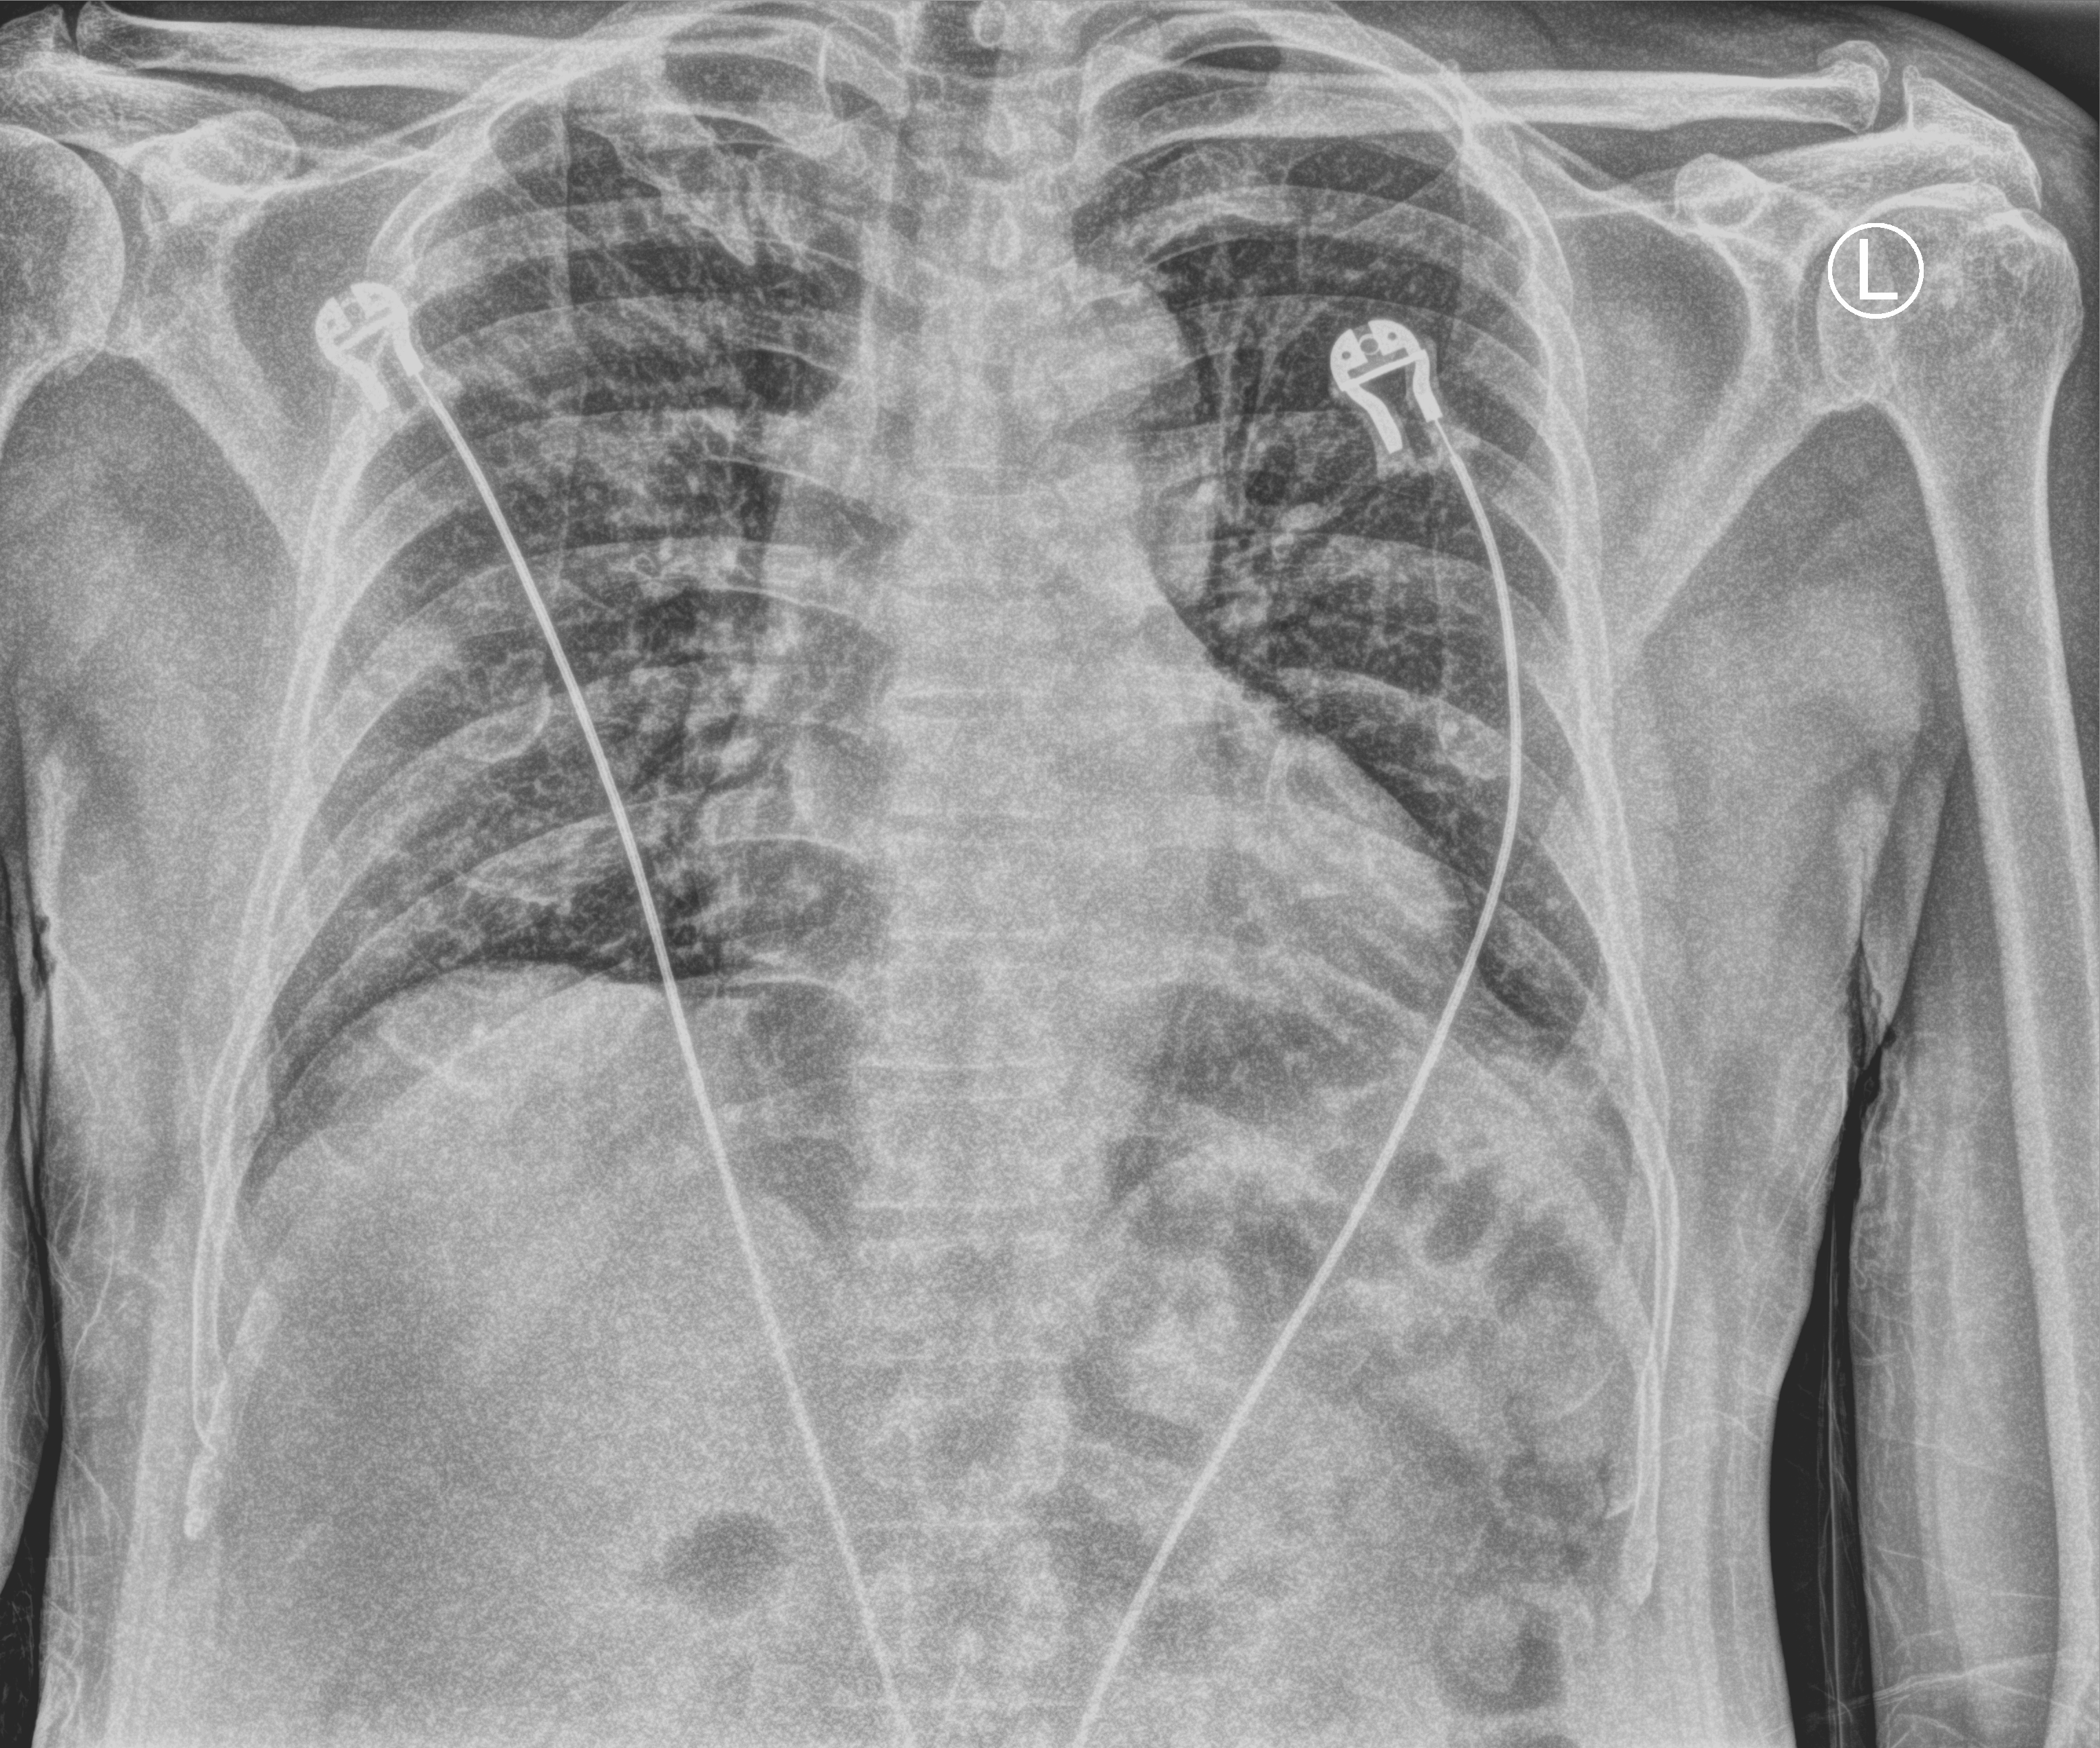
Chest X-ray (portable), anteroposterior (AP) projection. Patient hospitalised with COVID-19; male, aged 60–74 years.
From the hospital-stay record, not from the radiograph (when in the stay this image was taken is not recorded): admitted to intensive care during this hospital stay: no.